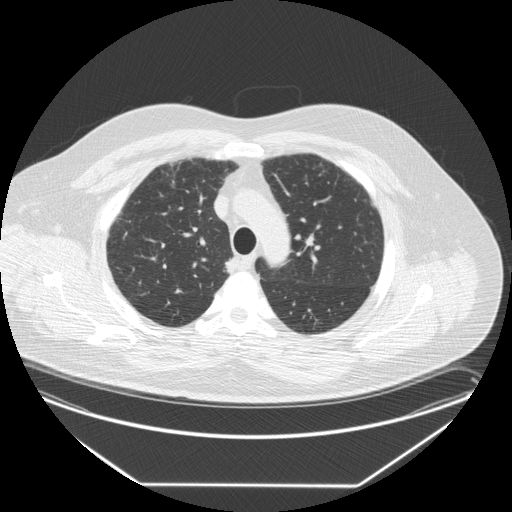
Axial slice from a low-dose chest CT screening exam, third annual screen, lung window (W 1500 / L -600 HU), 2.5 mm slice thickness, standard (soft-tissue) reconstruction kernel (STANDARD), 120 kVp, 512 × 512 image matrix, field of view 440 × 440 mm. Male, age 58 years at enrolment.
- Expert reader's lesion annotation, bounding box (x1, y1, x2, y2) in pixels: (216, 251, 251, 287).
- The exam's reader record, not a measurement of the box and not confirmed to be the same lesion: non-calcified nodule or mass ≥4 mm, right upper lobe, 15 × 12 mm, smooth margins, soft tissue attenuation, pre-existing on the prior screen: no.
- Official screen result: positive, other.
- Participant outcome: lung cancer diagnosed 17 days after this screen — large cell carcinoma, NOS, right upper lobe, stage IV (AJCC 6th edition), 35 mm at pathology.